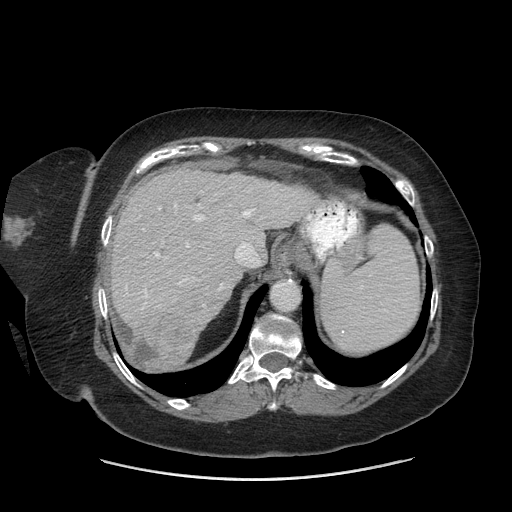
Contrast-enhanced abdominal CT (liver protocol), one axial slice; position 55 of 69 along the scan axis; 140 kVp; soft-tissue window (W 400 / L 40 HU); 2.5 mm slice thickness; 512 × 512 image matrix, field of view 420 × 420 mm. From the clinical record (not read from this slice): diagnosis: hepatocellular carcinoma (patient treated with transarterial chemoembolisation; whether this scan precedes or follows treatment is not stated here); TNM stage (as recorded): Stage-IIIB; Child-Pugh class: A; tumour differentiation: moderately differentiated; tumour nodularity: multinodular.
Outlined on this slice (semi-automatically segmented with operator editing):
- liver parenchyma outside the tumour (the mass and vessels are separate outlines, so this box may not span the whole liver): bounding box (x1, y1, x2, y2) in pixels: (110, 168, 319, 370)
- mass: (131, 309, 195, 368)
- liver vessels: (125, 205, 260, 306)